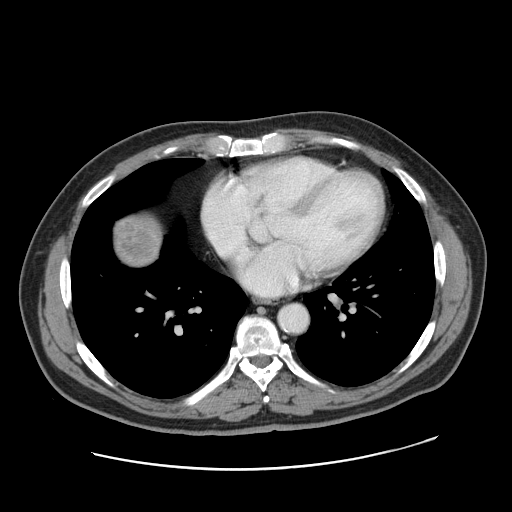
Contrast-enhanced abdominal CT, one axial slice. Slice 167 of 178 in the series (ordered by position). 120 kVp. Intravenous contrast given. Soft-tissue window (W 400 / L 40 HU). 512 × 512 image matrix. Male patient, age 63 years. From the clinical record (not read from this slice): diagnosis: colorectal cancer liver metastases, imaged before liver resection; multiple liver metastases: yes; largest metastasis: 8 cm; disease in both lobes: yes.
Structures marked on this image (outlined manually by an expert reader):
- liver: bounding box (x1, y1, x2, y2) in pixels: (113, 215, 161, 266)
- liver metastasis: (116, 217, 161, 265)